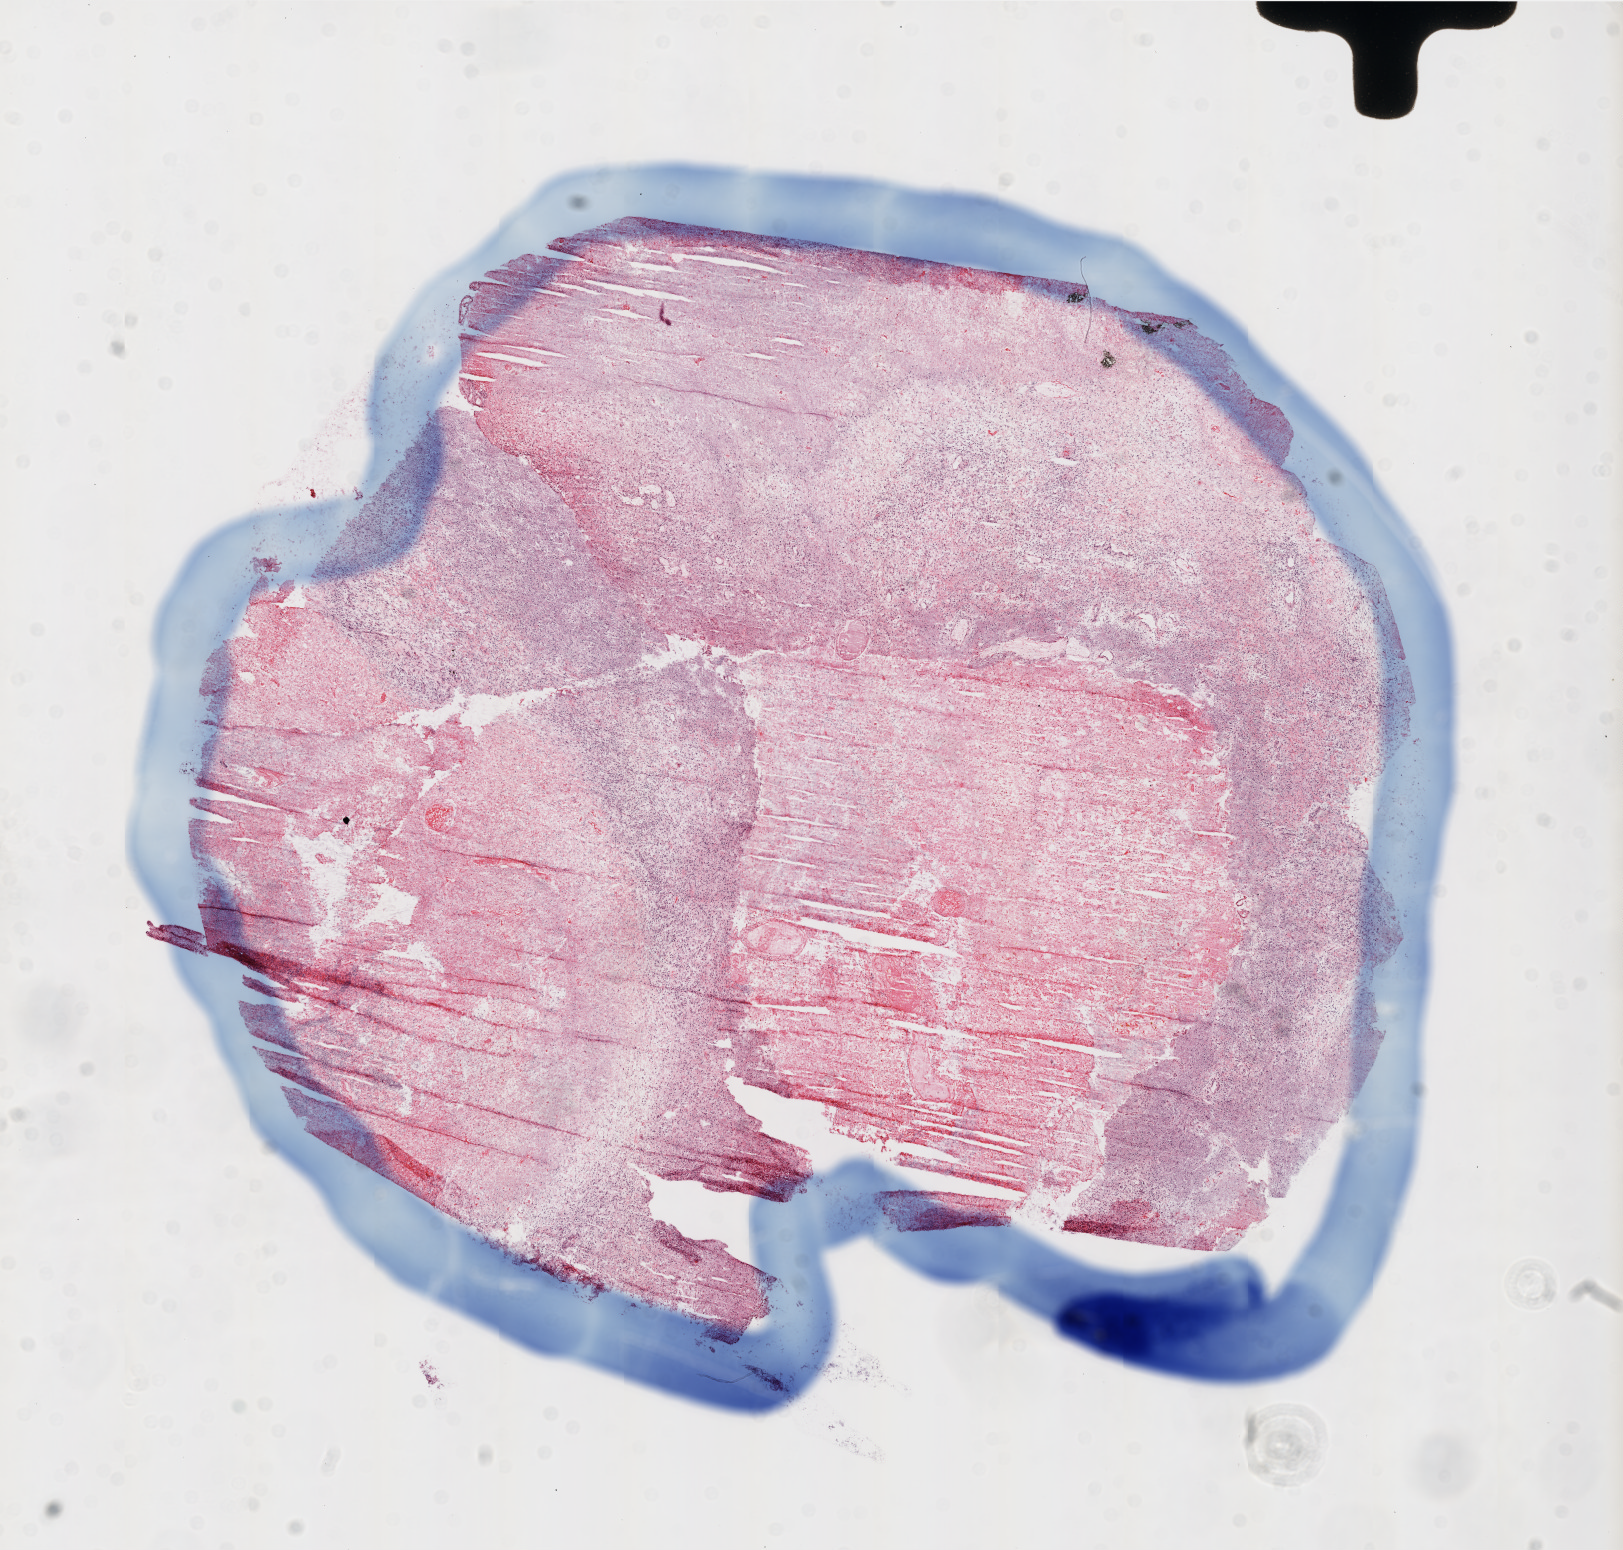
Whole-slide histology image, H&E-stained — a low-resolution overview of the entire scanned area, about 13.0 x 12.4 mm (acquisition: 20x scan), frozen section from the top of the tissue portion, primary tumour sample from the brain. Male patient; age at initial diagnosis 40 years. Slide review estimates, as recorded: tumour cells 50%, tumour nuclei 95%, normal cells 0%, stromal cells 50%, necrosis 0%. Infiltration values recorded for this section: lymphocyte infiltration 0%, monocyte infiltration 0%, neutrophil infiltration 0%.
Histologic diagnosis: Glioblastoma.